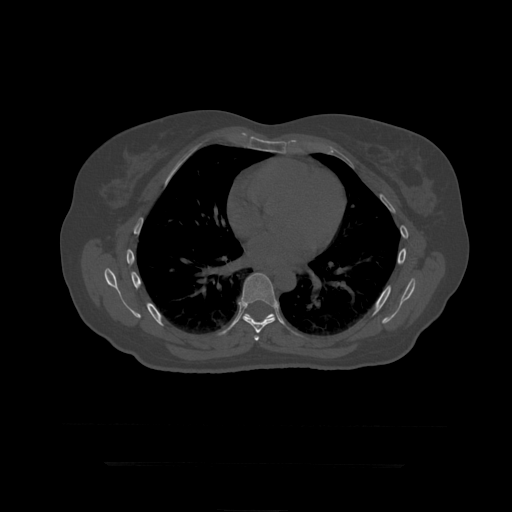
CT including the spine, one axial slice; slice 277 of 399 in the series (ordered by position); reconstruction kernel STANDARD; 120 kVp; bone window (W 1800 / L 400 HU); 512 × 512 image matrix. Patient age 41 years. Case-level facts recorded for this patient, not image findings: primary cancer: breast.
Outlined on this slice (semi-automatic segmentation, software-assisted and operator-edited):
- T7 vertebra: box from (x=254, y=336) to (x=260, y=341) px
- T8 vertebra: (x=241, y=273)–(x=276, y=334)
- T9 vertebra: (x=246, y=314)–(x=289, y=329)